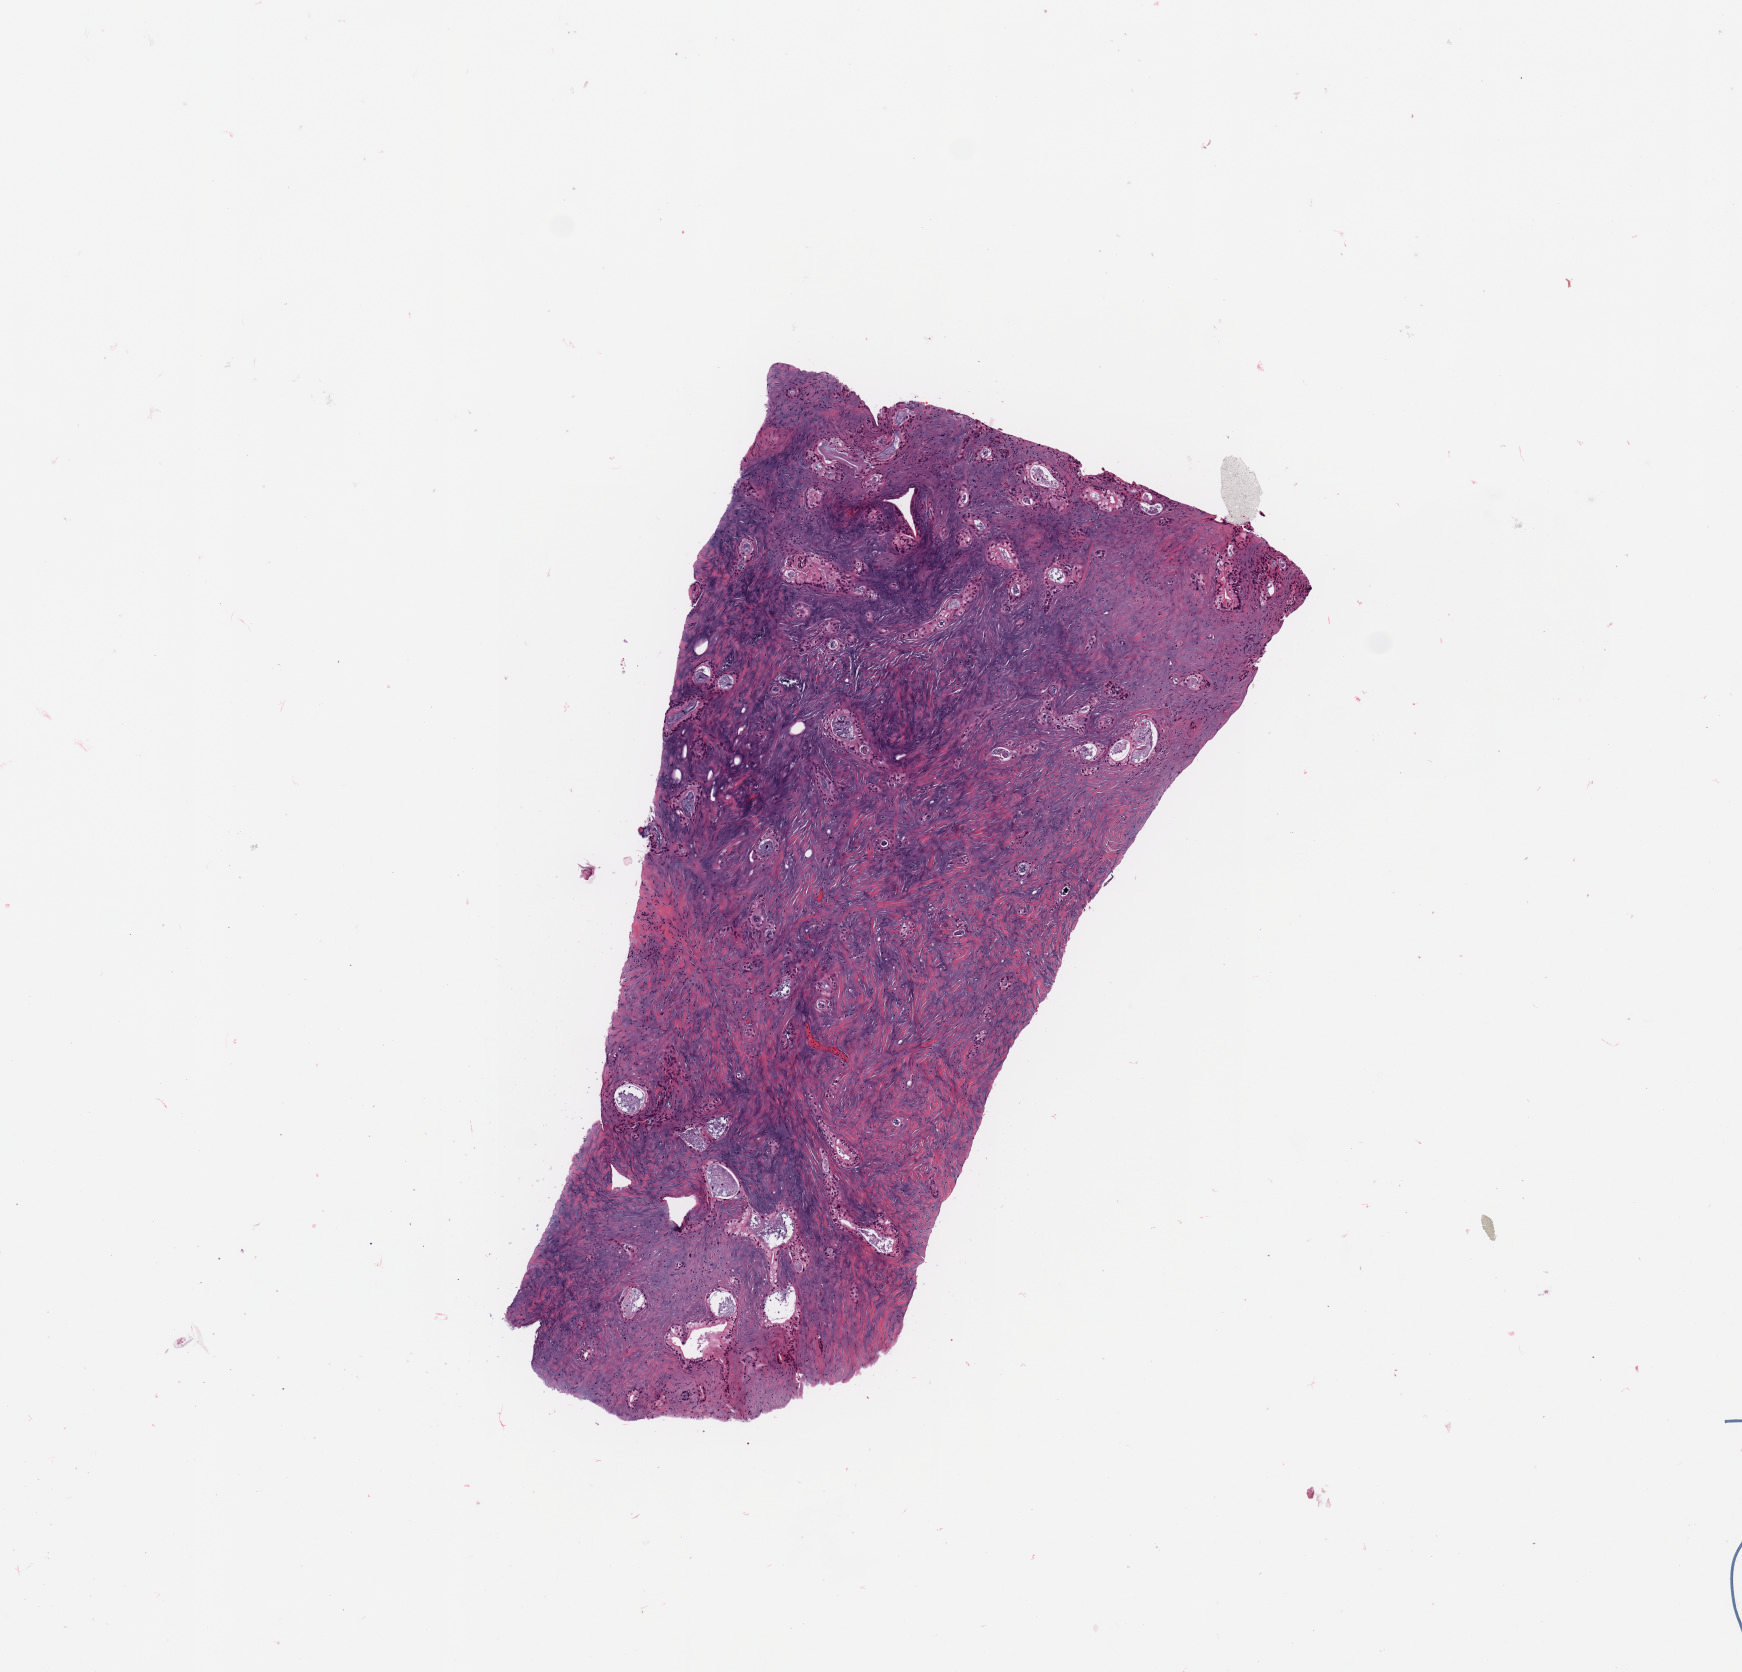
Whole-slide histology image, H&E-stained — a low-resolution overview of the entire scanned area, about 6.9 x 6.6 mm (acquisition: 20x scan). Tumour tissue sample, pancreas. Male, 84 y/o. Histologic grade: G2 (moderately differentiated).
- primary tumour site (as recorded): head
- histologic diagnosis: Infiltrating duct carcinoma, NOS
- AJCC pathologic stage: III